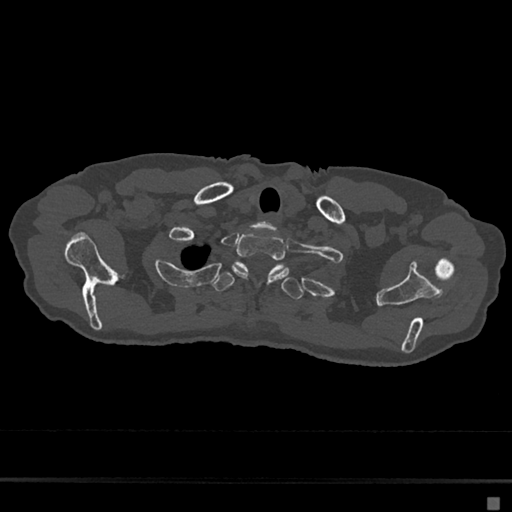
CT including the spine, one axial slice. Slice 597 of 797 in the series (ordered by position). Reconstruction kernel Br40s/3. 120 kVp. Bone window (W 1800 / L 400 HU). 0.5 mm slice thickness. 512 × 512 image matrix, field of view 360 × 360 mm. Patient: female, 68 years. Case-level facts recorded for this patient, not image findings: primary cancer: renal.
Outlined on this slice (semi-automatic segmentation, software-assisted and operator-edited):
- T1 vertebra: bounding box (x1, y1, x2, y2) in pixels: (232, 233, 290, 282)
- T2 vertebra: (212, 262, 304, 299)